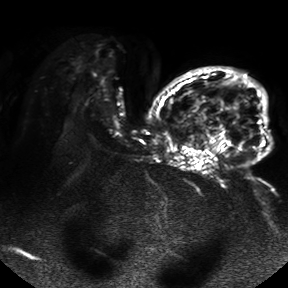
Breast MRI, one axial slice; slice 26 of 50 in the series (ordered by position); diffusion-weighted series; image 2 of 4 stored at this slice position (different b-values; order by instance number); 1.5 T; 4 mm slice thickness; 288 × 288 image matrix, field of view 390 × 390 mm. Female patient.
Structures marked on this image (expert manual segmentation):
- tumour on diffusion-weighted imaging: bounding box <218,96,247,146> (left, top, right, bottom; pixels)